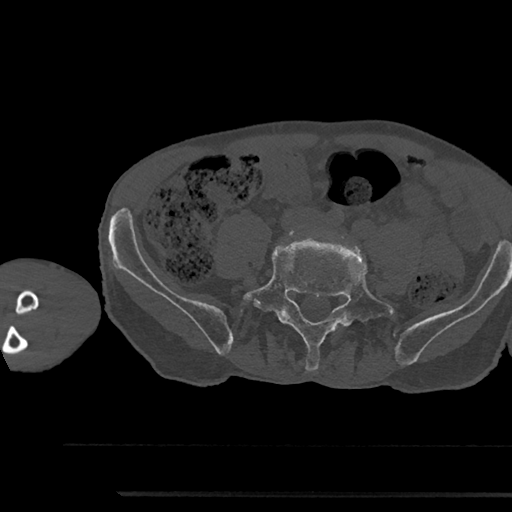
CT including the spine, one axial slice; reconstruction kernel Br40s/3; 120 kVp; bone window (W 1800 / L 400 HU); 0.5 mm slice thickness; 512 × 512 image matrix. Male patient, age 79 years. From the clinical record (not read from this slice): primary cancer: prostate.
Structures marked on this image (semi-automatically segmented with operator editing):
- L5 vertebra: box from (x=241, y=238) to (x=396, y=371) px